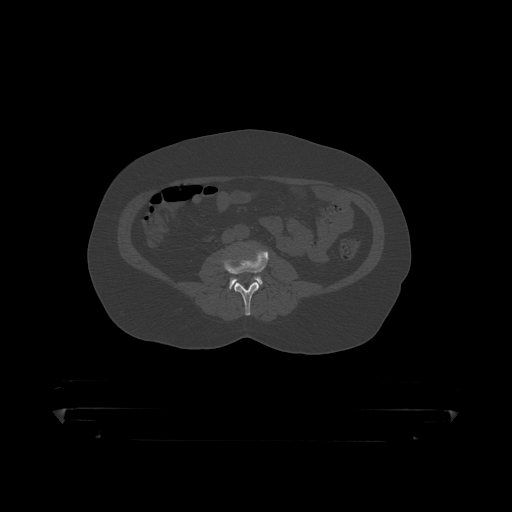
CT including the spine, one axial slice. Position 82 of 390 along the scan axis. Bone window (W 1800 / L 400 HU). 512 × 512 image matrix, field of view 650 × 650 mm. Patient: male, 60 years. From the clinical record (not read from this slice): primary cancer: prostate.
Annotated regions visible in this slice (semi-automatic segmentation, software-assisted and operator-edited):
- L3 vertebra: bounding box [x1, y1, x2, y2] px = [222, 246, 269, 316]
- L4 vertebra: [230, 276, 263, 289]